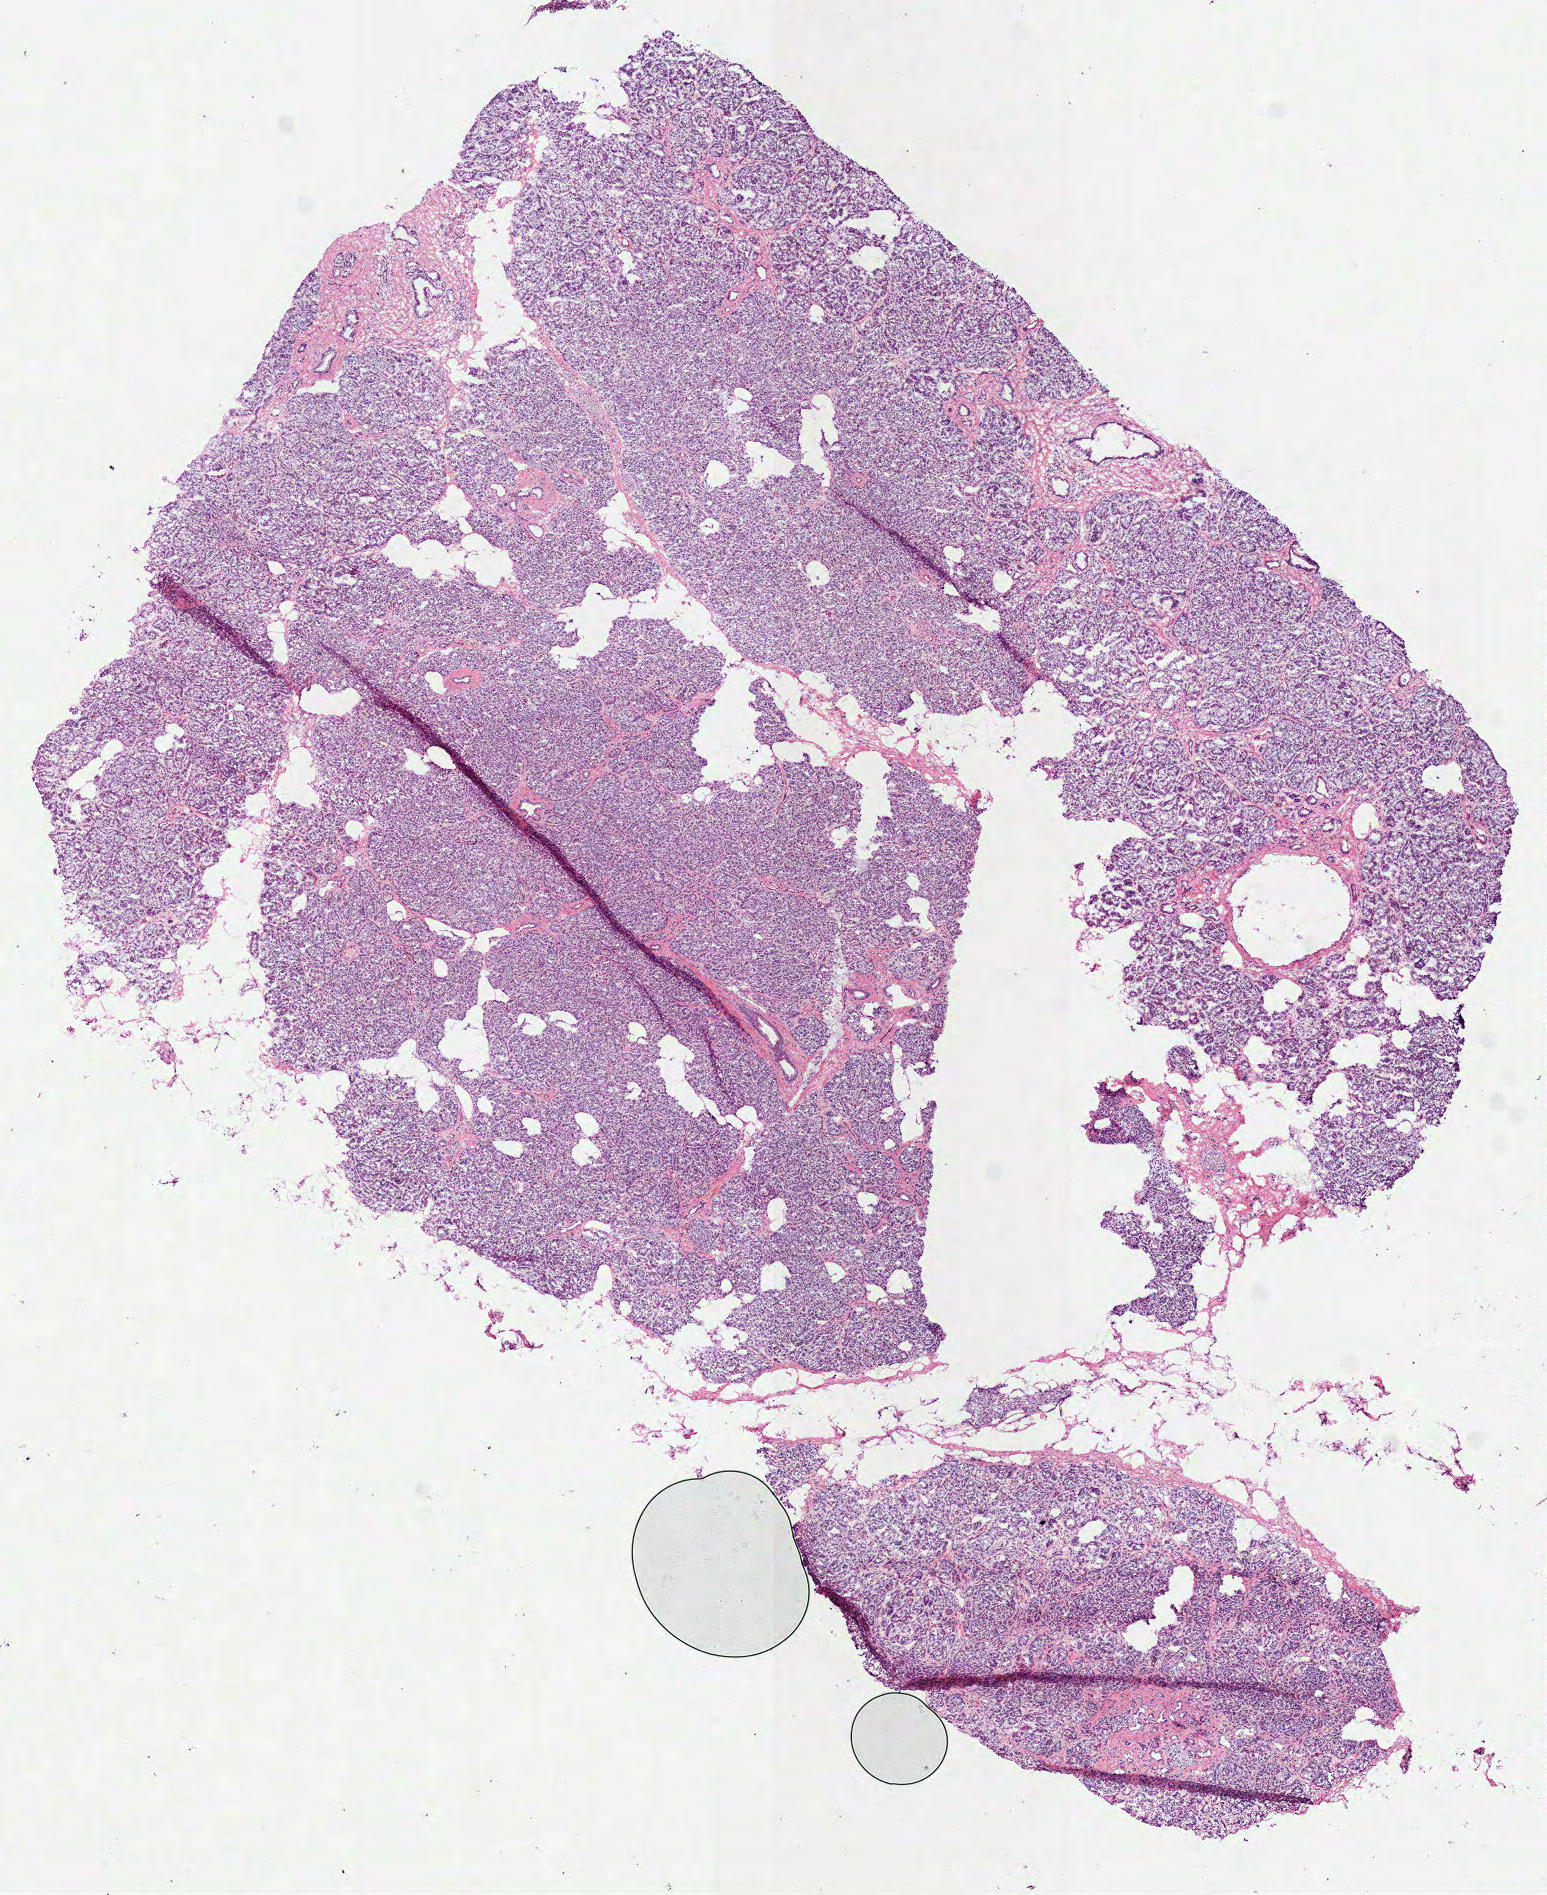
H&E whole-slide image — whole scanned area (about 6.1 x 7.5 mm, from a 40x scan) shown as a low-resolution overview, frozen section, pancreas, primary tumour sample. Male patient; age at initial diagnosis 70 years.
Histologic diagnosis: Adenocarcinoma, NOS (head of pancreas).